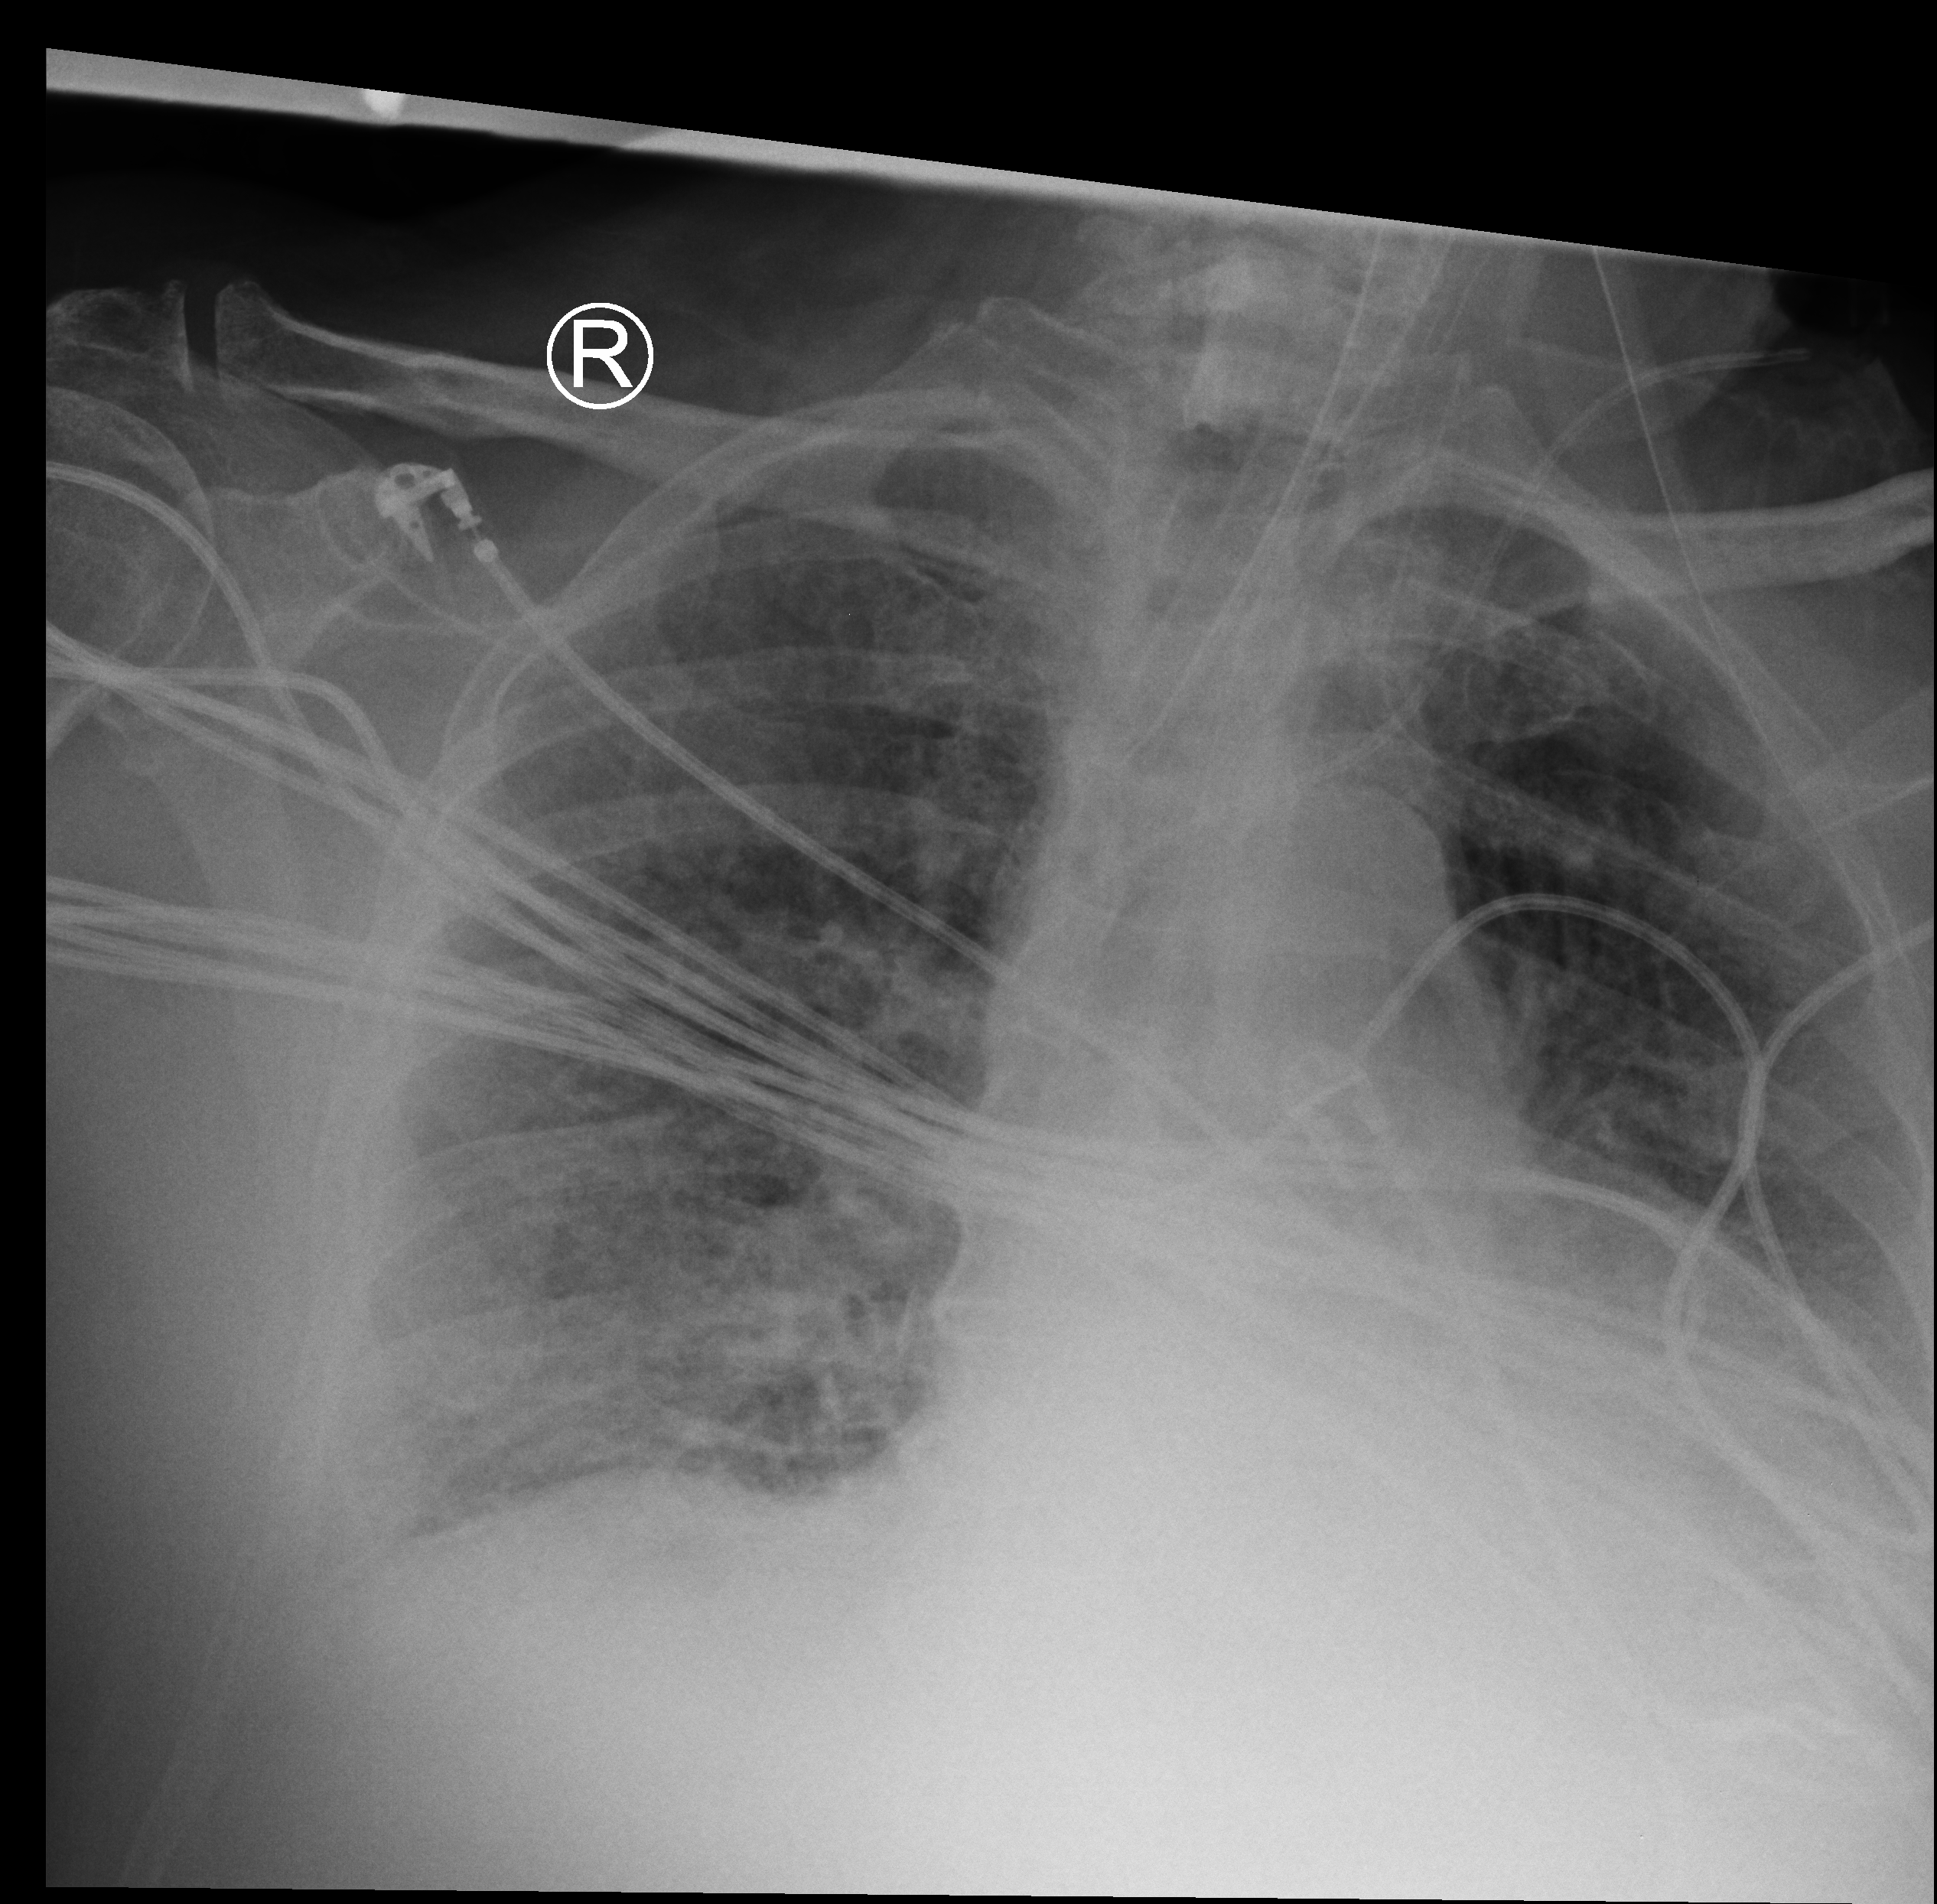
Chest X-ray (portable), anteroposterior (AP) projection. Patient hospitalised with COVID-19; male, aged 75–90 years.
Admission-level facts for this patient (not findings on this image; timing relative to this image not recorded):
- chronic kidney disease (admission record): no